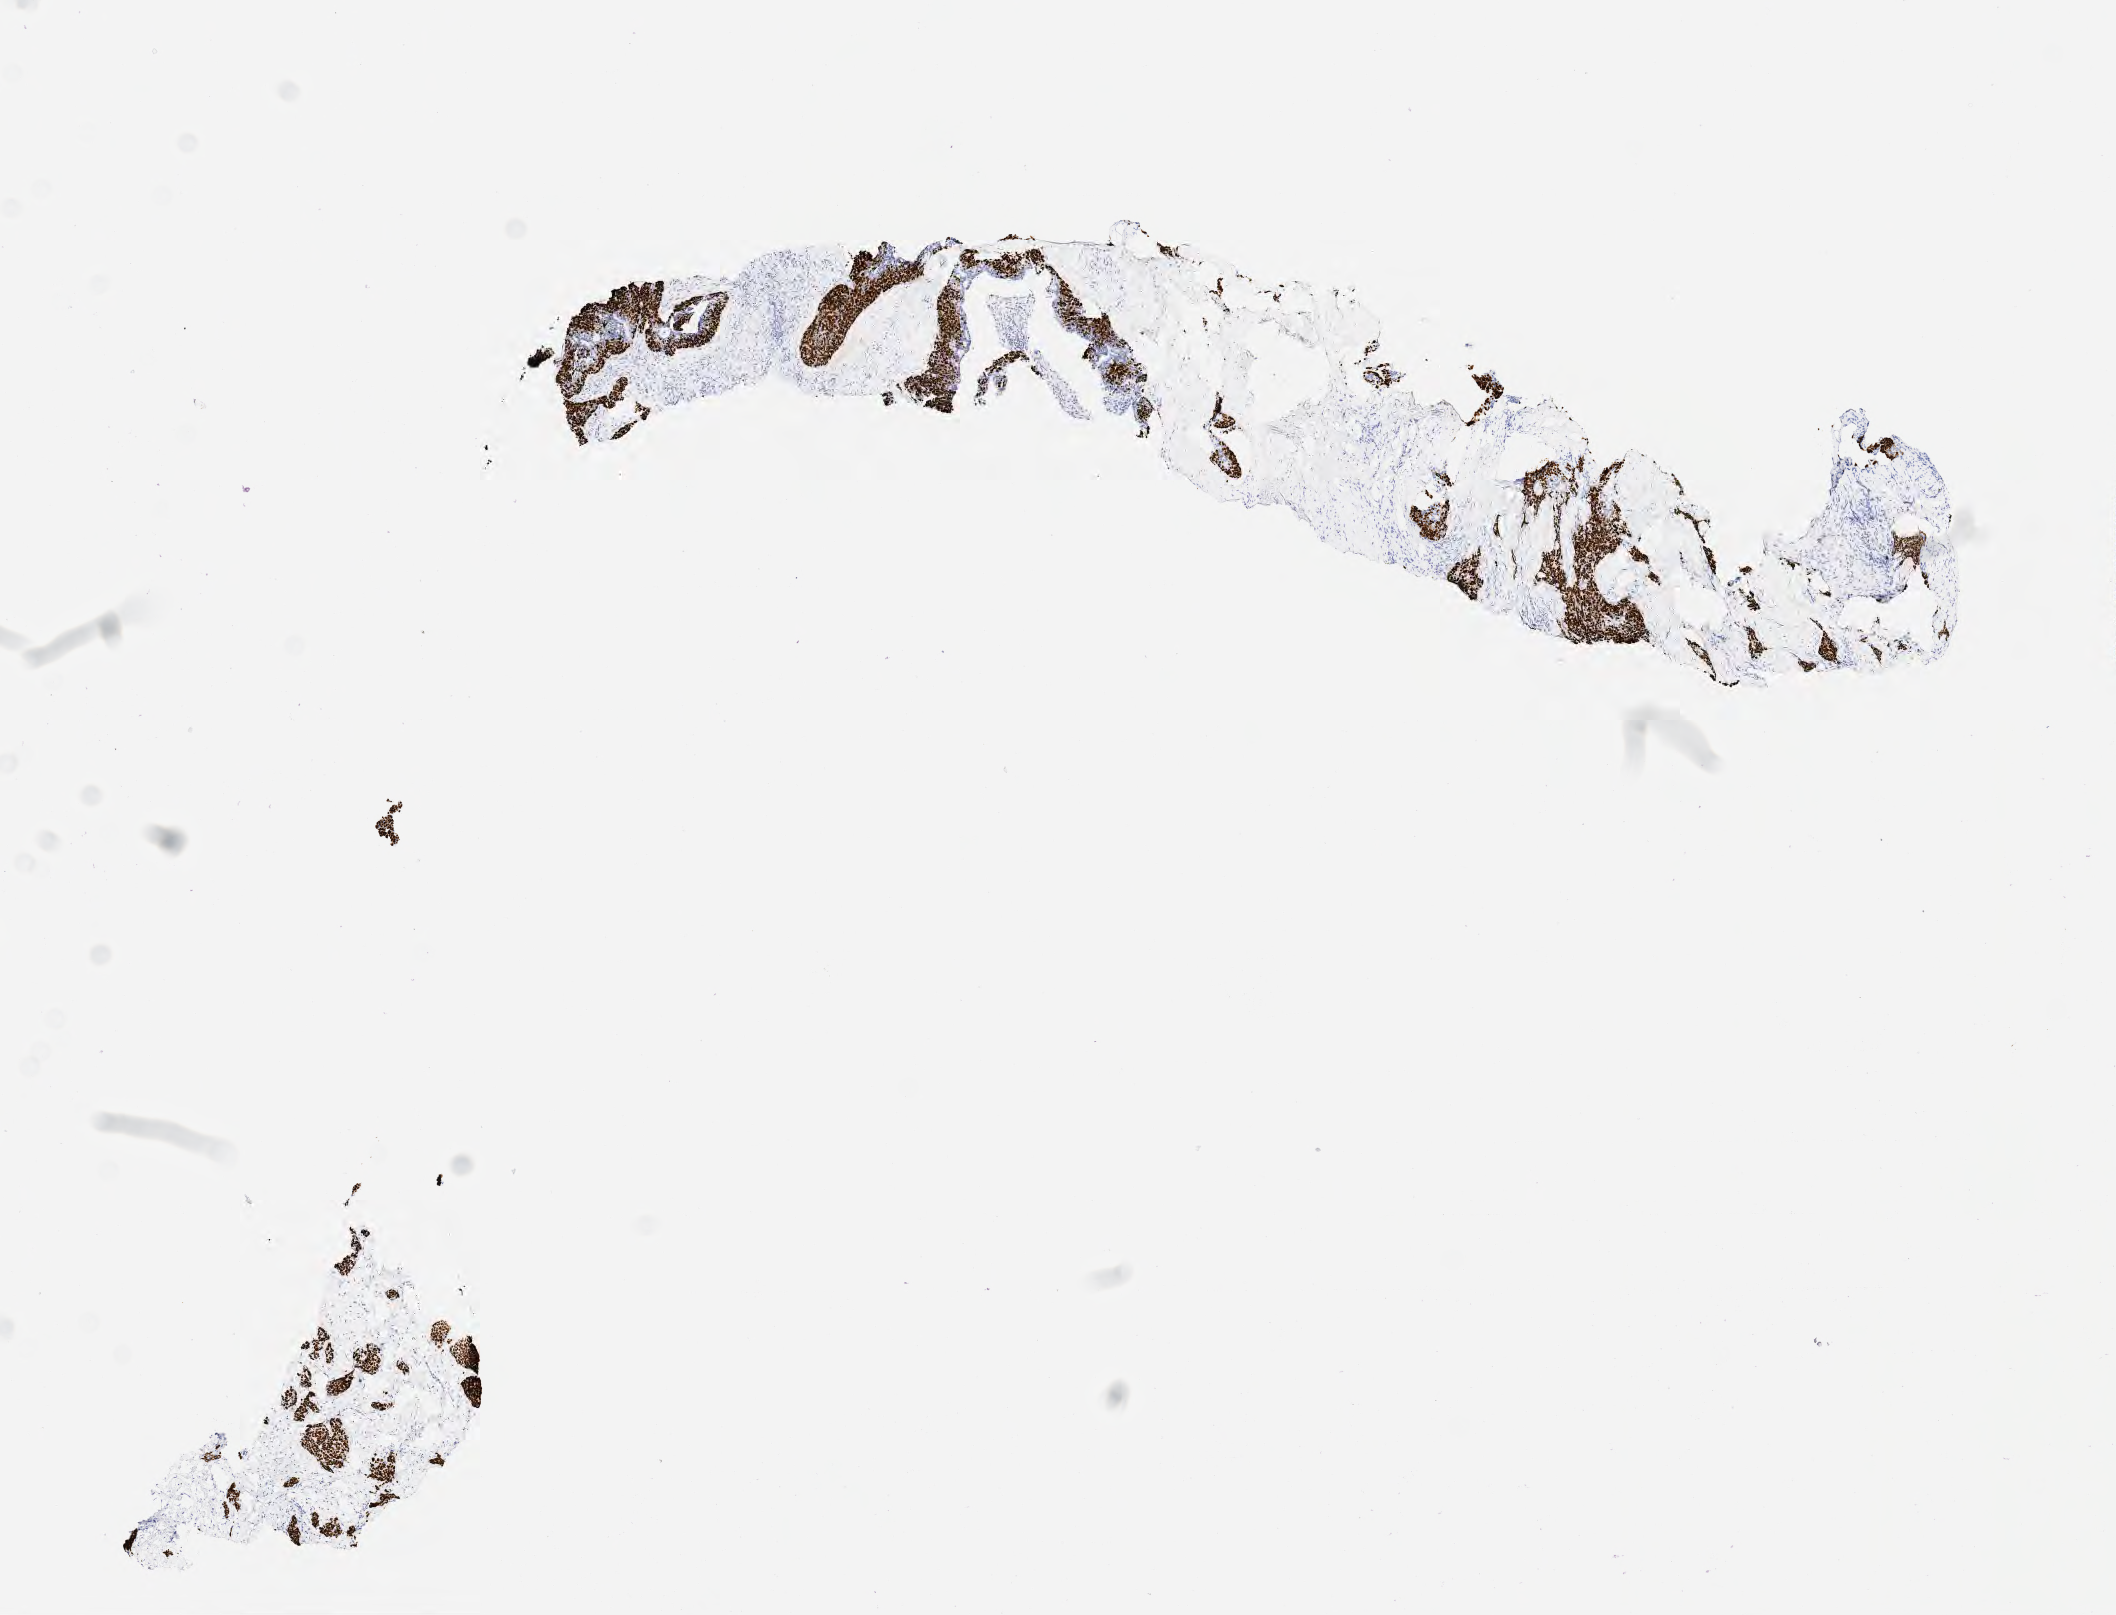
IHC for p40, whole-slide image, low-resolution overview of the scanned area, about 8.6 x 6.5 mm. Specimen: tumor tissue. Anatomic site: lung. Patient: female, 68 years old.
- histologic diagnosis: Squamous cell carcinoma, large cell, nonkeratinizing, NOS